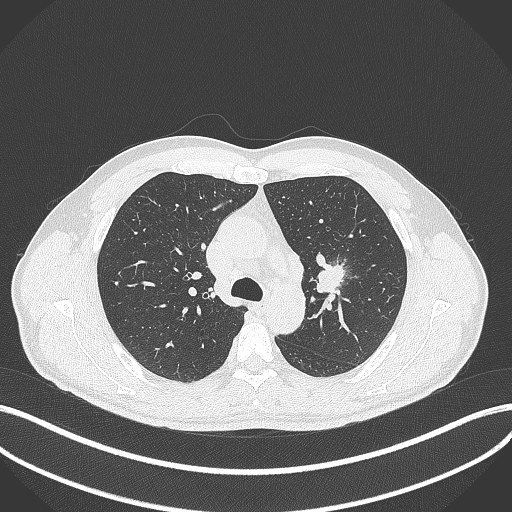
Chest CT, one axial slice. Slice 290 of 392 in the series (ordered by position). Reconstruction kernel B70f. 120 kVp. Lung window (W 1500 / L -600 HU). 1 mm slice thickness. 512 × 512 image matrix. Male patient, age 50 years. Case-level facts recorded for this patient, not image findings: clinical TNM (as recorded): T1c N1 M1b.
Outlined on this slice (rectangle marked by the reading radiologist):
- lung tumour (recorded histology: squamous cell carcinoma): bounding box [x1, y1, x2, y2] px = [316, 258, 345, 297]